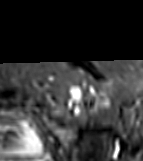
MRI of an extremity soft-tissue mass, one axial slice. Position 63 of 81 along the scan axis. STIR. MR volume resampled by the dataset authors to the PET/CT grid (not the native acquisition matrix). 3.27 mm slice thickness. 143 × 161 image matrix. Female patient. Case-level facts recorded for this patient, not image findings: histological type: myxofibrosarcoma; grade: intermediate; site of the primary tumour: left thigh.
Outlined on this slice (expert contour drawn on MRI and transferred to this co-registered scan by the dataset authors):
- gross tumour volume including surrounding oedema: bounding box <69,90,84,107> (left, top, right, bottom; pixels)